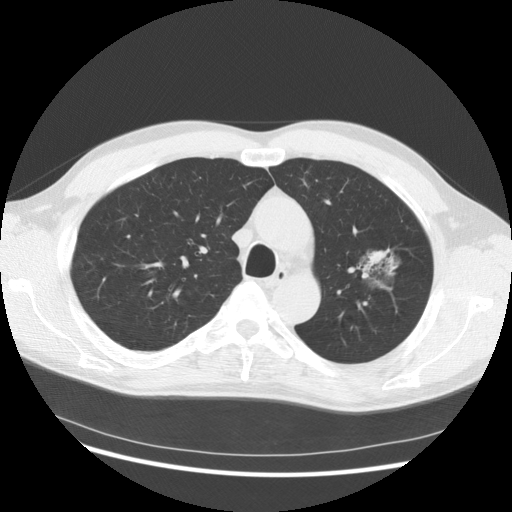
Axial slice from a low-dose chest CT screening exam, third screening round (two years after baseline), lung window (W 1500 / L -600 HU), 2.5 mm slice thickness, standard (soft-tissue) reconstruction kernel (STANDARD). Male, age 61 years at enrolment.
• Expert-annotated lung lesion, bounding box (x1, y1, x2, y2) in pixels: (332, 227, 413, 307).
• Reader record for this screening exam (exam-level; its link to the box is not recorded): non-calcified nodule or mass ≥4 mm, left upper lobe, 37 × 33 mm, poorly defined margins, mixed attenuation, pre-existing on the prior screen: yes; interval growth: yes.
• Lung cancer was diagnosed 361 days after this screen: bronchiolo-alveolar adenocarcinoma, NOS, left upper lobe, well differentiated (G1), stage IB (AJCC 6th edition), 44 mm at pathology.